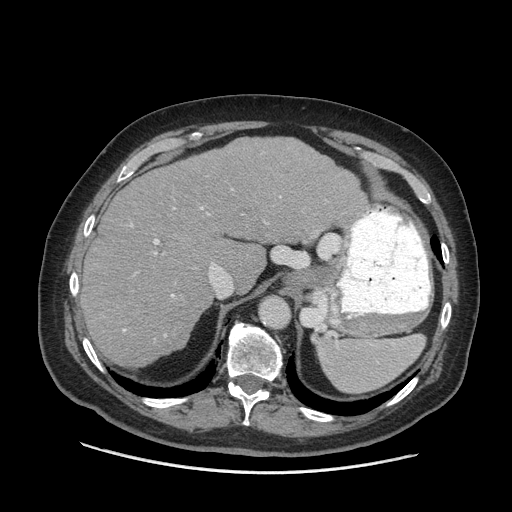
Contrast-enhanced abdominal CT (liver protocol), one axial slice. Slice 49 of 77 in the series (ordered by position). Reconstruction kernel STANDARD. 140 kVp. Soft-tissue window (W 400 / L 40 HU). 512 × 512 image matrix, field of view 420 × 420 mm. Case-level facts recorded for this patient, not image findings: diagnosis: hepatocellular carcinoma (patient treated with transarterial chemoembolisation; whether this scan precedes or follows treatment is not stated here); TNM stage (as recorded): Stage-I; Child-Pugh class: A; tumour nodularity: uninodular; tumour size: 3.8 cm.
Outlined on this slice (semi-automatic segmentation, software-assisted and operator-edited):
- liver parenchyma outside the tumour (the mass and vessels are separate outlines, so this box may not span the whole liver): box from (x=82, y=138) to (x=366, y=366) px
- liver vessels: (x=123, y=189)–(x=233, y=337)